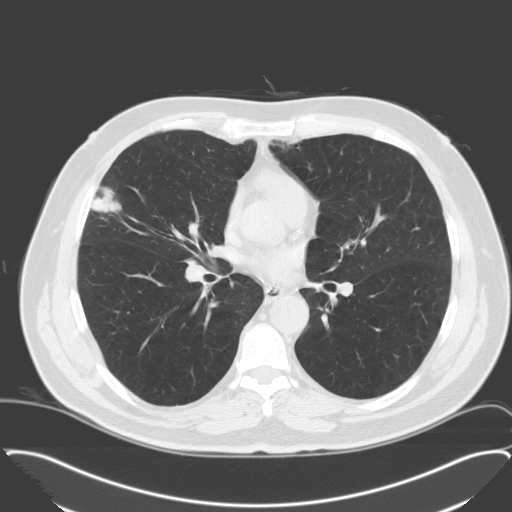
Low-dose screening chest CT, one axial slice; position 93 of 174 along the scan axis; lung window (W 1500 / L -600 HU); 3.2 mm slice thickness; 512 × 512 image matrix.
Structures marked on this image (outlined manually by an expert reader):
- lesion 1 (tumor, middle lobe of right lung): bounding box <92,188,121,212> (left, top, right, bottom; pixels)